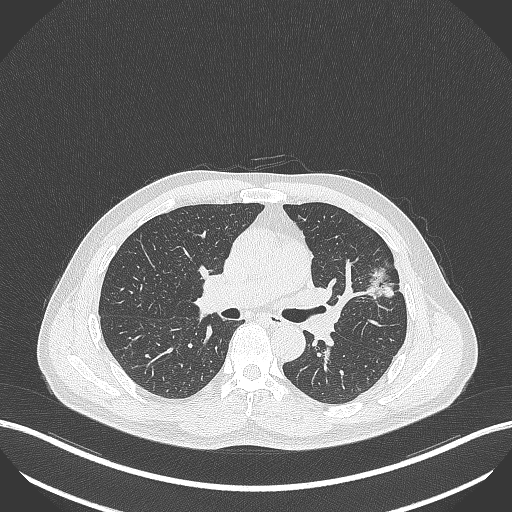
Chest CT, one axial slice; slice 230 of 418 in the series (ordered by position); reconstruction kernel B70f; 120 kVp; lung window (W 1500 / L -600 HU); 1 mm slice thickness; 512 × 512 image matrix, field of view 400 × 400 mm. Patient: male, 55 years. From the clinical record (not read from this slice): clinical TNM (as recorded): T1c N0 M0; histopathological grade: G2-3.
Annotated regions visible in this slice (bounding box drawn by a radiologist):
- lung tumour (recorded histology: adenocarcinoma): bounding box (x1, y1, x2, y2) in pixels: (366, 266, 394, 298)